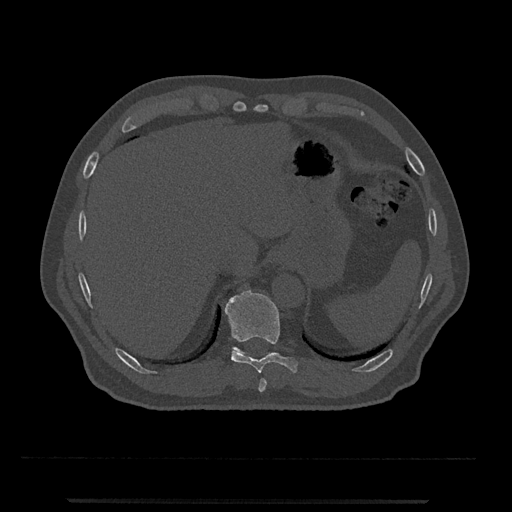
CT including the spine, one axial slice. Slice 512 of 797 in the series (ordered by position). Bone window (W 1800 / L 400 HU). 0.5 mm slice thickness. 512 × 512 image matrix, field of view 419 × 419 mm. Male patient, age 63 years. Case-level facts recorded for this patient, not image findings: primary cancer: prostate.
Structures marked on this image (semi-automatic segmentation, software-assisted and operator-edited):
- T10 vertebra: bounding box (x1, y1, x2, y2) in pixels: (224, 290, 299, 373)
- T11 vertebra: (232, 347, 270, 355)
- T9 vertebra: (258, 379, 267, 392)